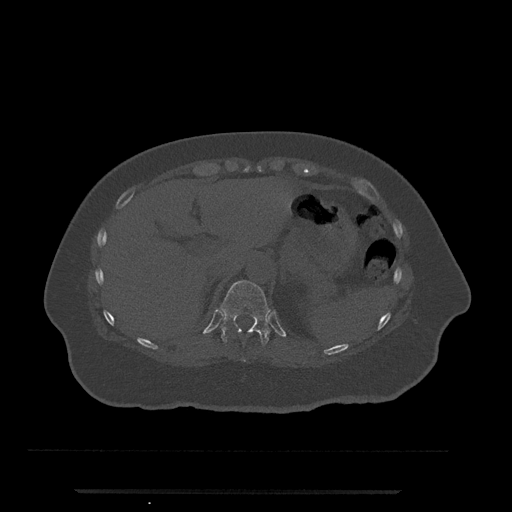
CT including the spine, one axial slice; slice 243 of 797 in the series (ordered by position); 120 kVp; bone window (W 1800 / L 400 HU); 0.5 mm slice thickness; 512 × 512 image matrix, field of view 440 × 440 mm. Patient: female, 51 years. From the clinical record (not read from this slice): primary cancer: neuro.
Annotated regions visible in this slice (semi-automatic segmentation, software-assisted and operator-edited):
- T10 vertebra: bounding box <243,359,246,362> (left, top, right, bottom; pixels)
- T11 vertebra: <219,280,272,346>